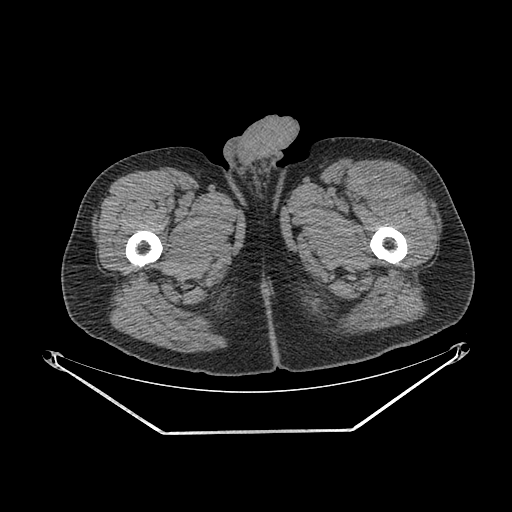
CT of an extremity soft-tissue mass (from a PET/CT study), one axial slice. Slice 260 of 267 in the series (ordered by position). Reconstruction kernel SOFT. 140 kVp. Soft-tissue window (W 400 / L 40 HU). 3.75 mm slice thickness. 512 × 512 image matrix, field of view 500 × 500 mm. Male patient. Case-level facts recorded for this patient, not image findings: histological type: extraskeletal osteosarcoma; grade: high; site of the primary tumour: thigh.
Annotated regions visible in this slice (expert contour drawn on MRI and transferred to this co-registered scan by the dataset authors):
- gross tumour volume (mass): bounding box [x1, y1, x2, y2] px = [377, 173, 417, 193]